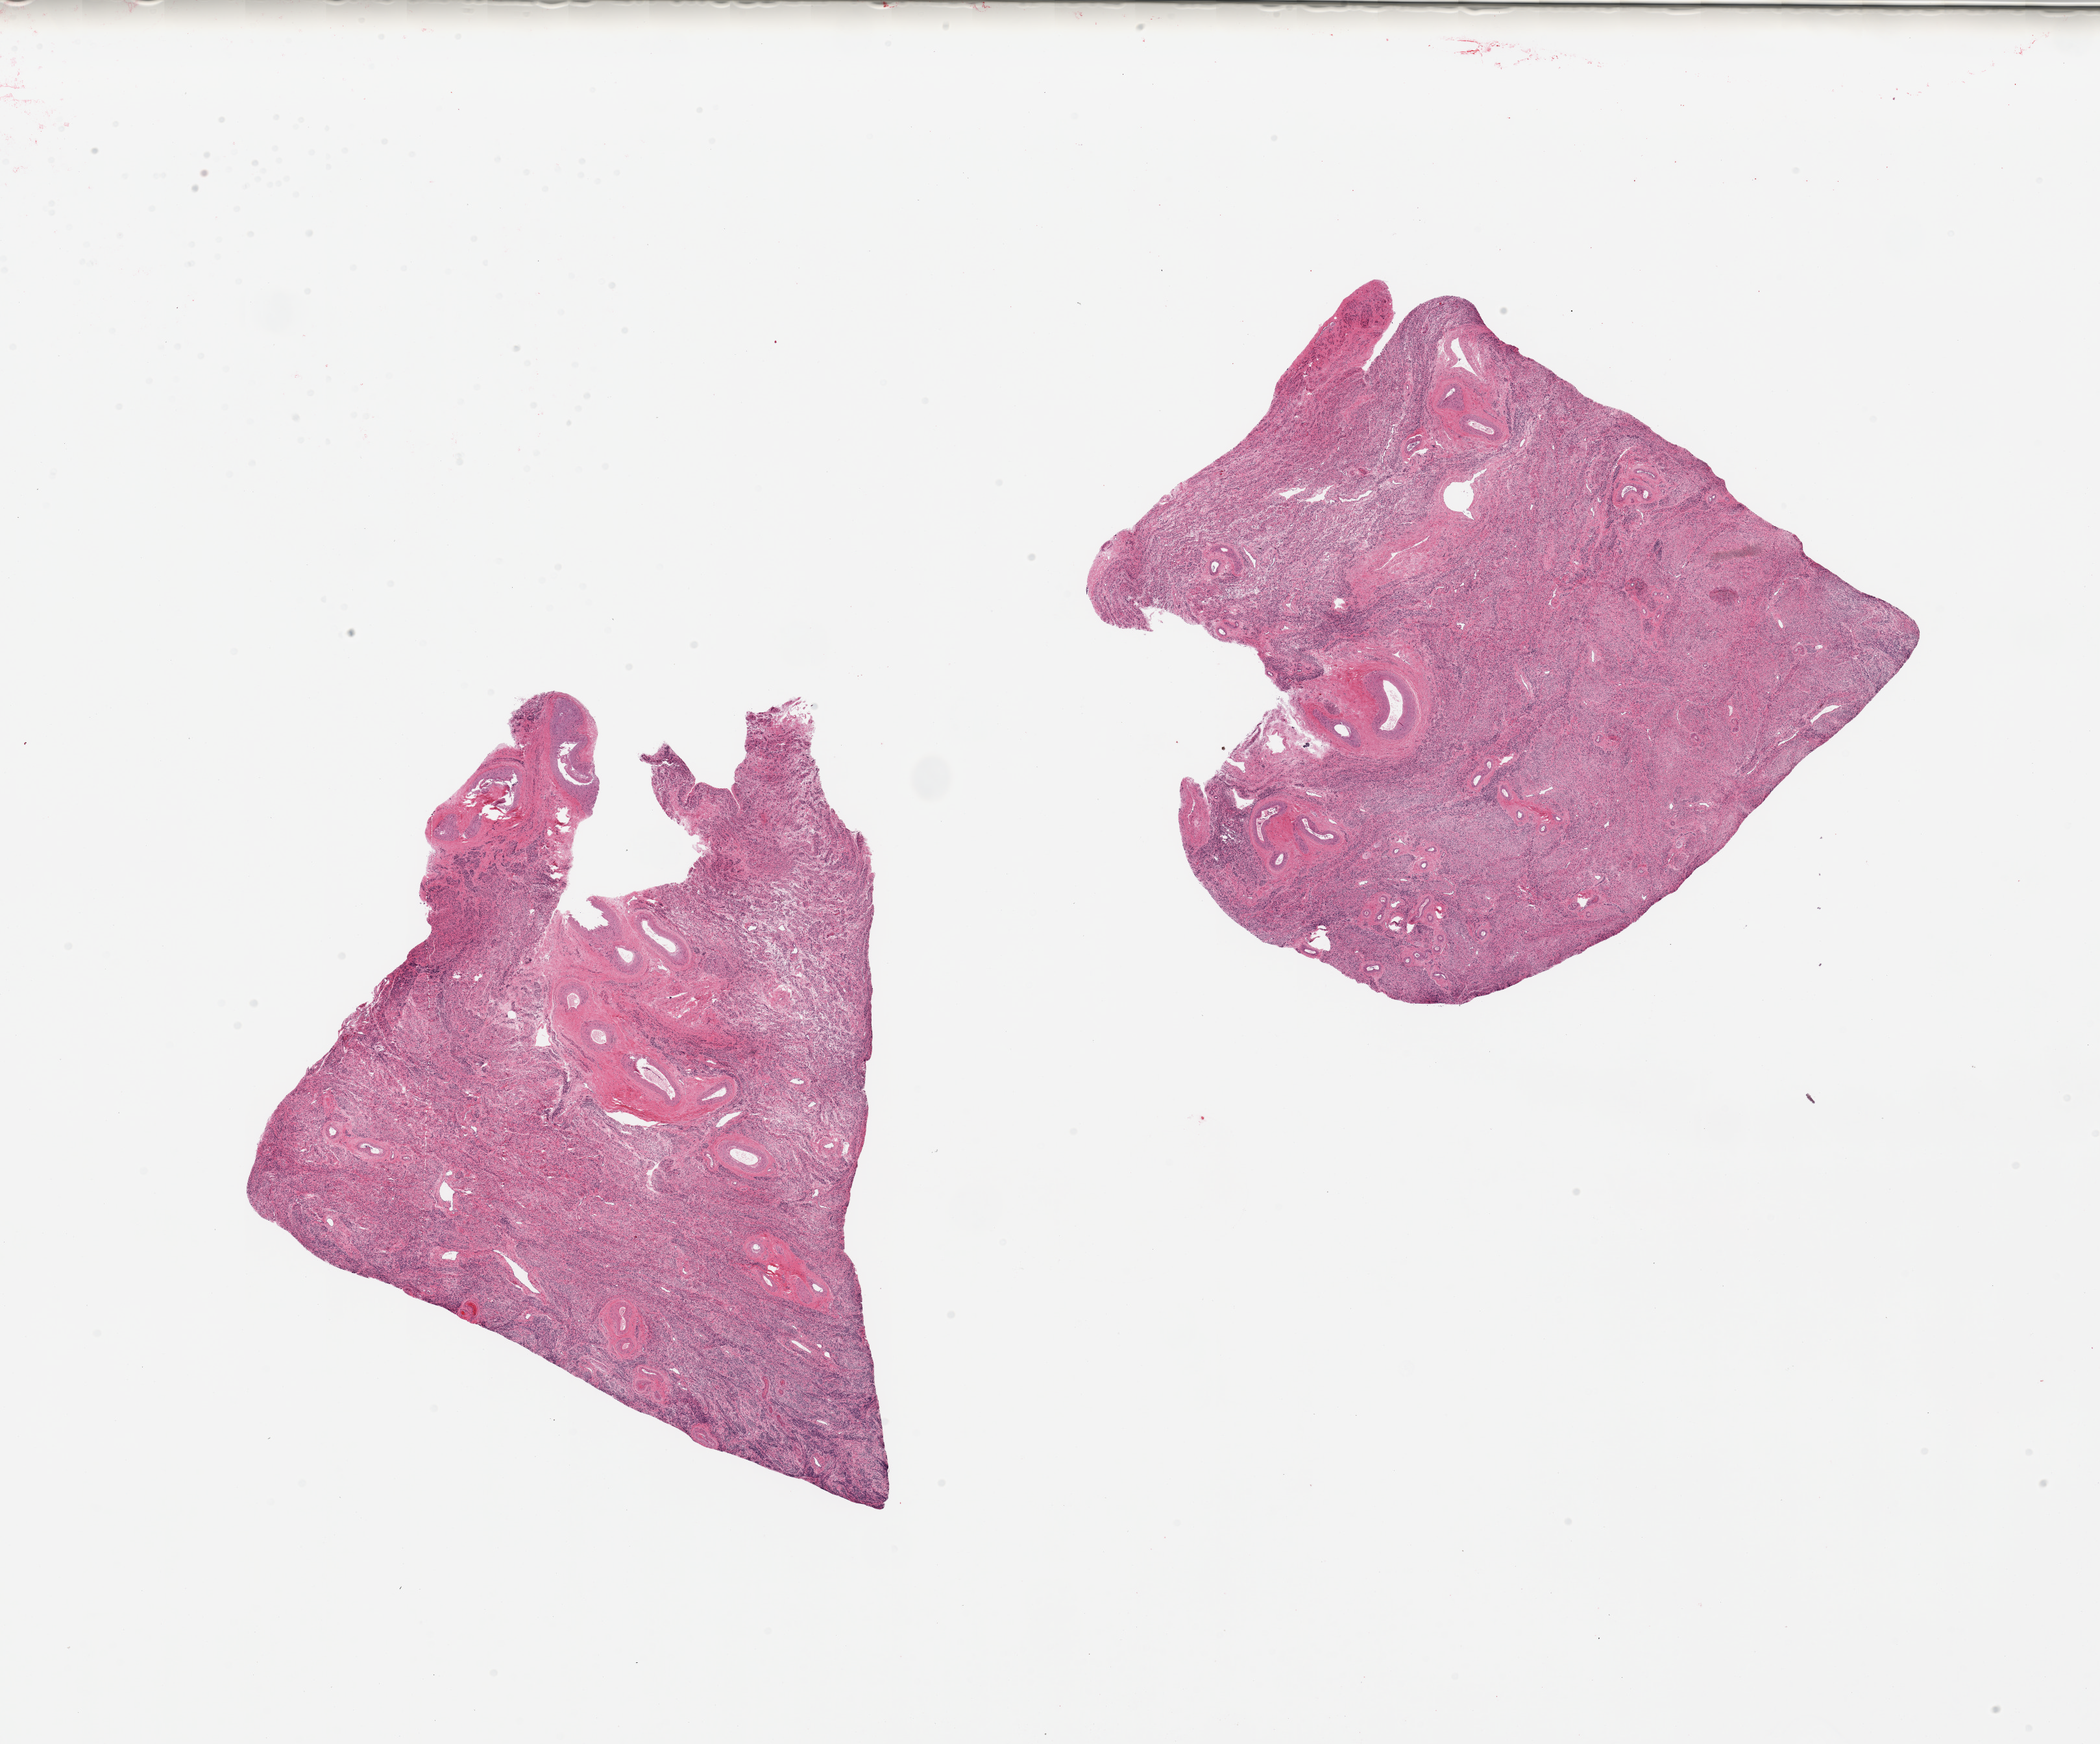
Whole-slide image, H&E stain, shown as a low-resolution overview of the whole scanned area (about 25.6 x 21.3 mm); PAXgene-fixed paraffin-embedded (PFPE) section; sampled site (target tissue): uterus; tissue donor sample. Donor: female.
• review note (as recorded): 2 pieces, myometrium only